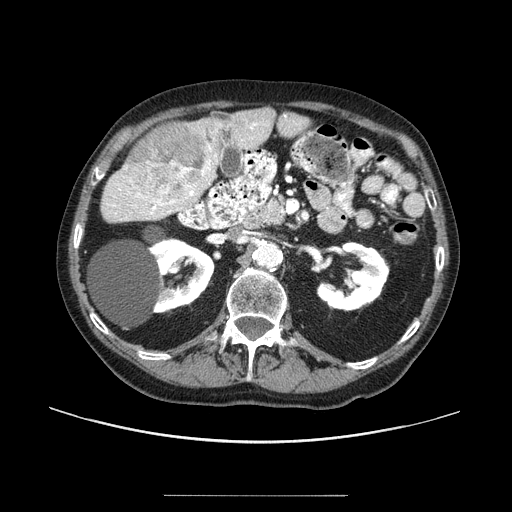
Contrast-enhanced abdominal CT (liver protocol), one axial slice; position 39 of 91 along the scan axis; 100 kVp; one of 2 acquisitions stored at this slice position; soft-tissue window (W 400 / L 40 HU); 512 × 512 image matrix. From the clinical record (not read from this slice): diagnosis: hepatocellular carcinoma (patient treated with transarterial chemoembolisation; whether this scan precedes or follows treatment is not stated here); TNM stage (as recorded): Stage-I; Child-Pugh class: A; tumour differentiation: moderately differentiated.
Annotated regions visible in this slice (semi-automatically segmented with operator editing):
- liver parenchyma outside the tumour (the mass and vessels are separate outlines, so this box may not span the whole liver): box from (x=100, y=108) to (x=274, y=222) px
- mass: (x=122, y=122)–(x=215, y=203)
- liver vessels: (x=109, y=123)–(x=258, y=215)